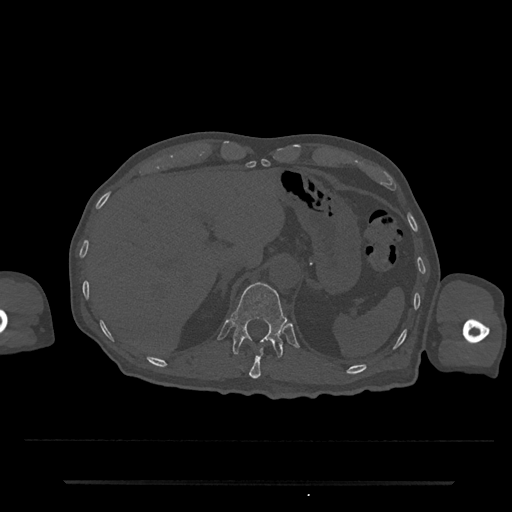
CT including the spine, one axial slice. Slice 215 of 797 in the series (ordered by position). 120 kVp. Bone window (W 1800 / L 400 HU). 0.5 mm slice thickness. 512 × 512 image matrix, field of view 427 × 427 mm. Patient: male, 74 years. Case-level facts recorded for this patient, not image findings: primary cancer: prostate.
Structures marked on this image (semi-automatic segmentation, software-assisted and operator-edited):
- T11 vertebra: bounding box (x1, y1, x2, y2) in pixels: (249, 348, 264, 379)
- T12 vertebra: (231, 282, 288, 358)